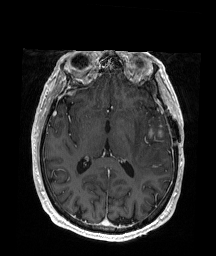
Brain MRI from a brain-tumour surgery series, one axial slice; position 95 of 176 along the scan axis; T1-weighted post-contrast; 1 mm slice thickness; 216 × 256 image matrix. Case-level facts recorded for this patient, not image findings: histopathology: Glioblastoma; WHO grade: 4; IDH mutation: no; tumour location: Left Frontal.
Annotated regions visible in this slice (manually delineated by an expert):
- tumour: bounding box [x1, y1, x2, y2] px = [149, 129, 164, 137]